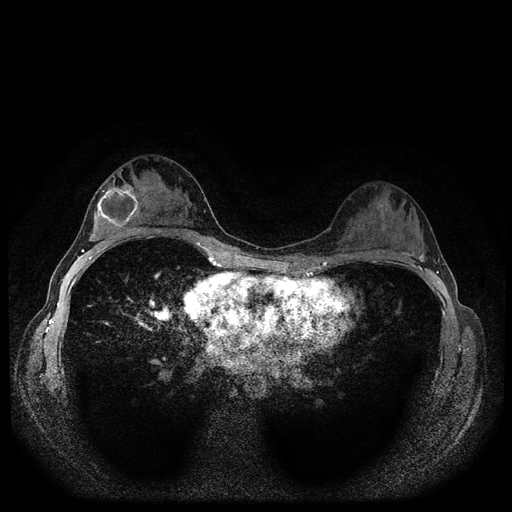
Breast MRI (dynamic contrast-enhanced, multi-phase), one axial slice. Slice 62 of 116 in the series (ordered by position). Dynamic contrast-enhanced series, time point 2 of 5 at this slice position (early post-contrast). 1.5 T. TE 2.7 ms, TR 5.4 ms. 2 mm slice thickness. 512 × 512 image matrix, field of view 320 × 320 mm. Female patient, age 29 years.
Structures marked on this image (semi-automatic segmentation, software-assisted and operator-edited):
- breast lesion (labelled 'tumour' in the annotation; benign lesions carry a separate 'benign' label): bounding box (x1, y1, x2, y2) in pixels: (96, 182, 141, 232)